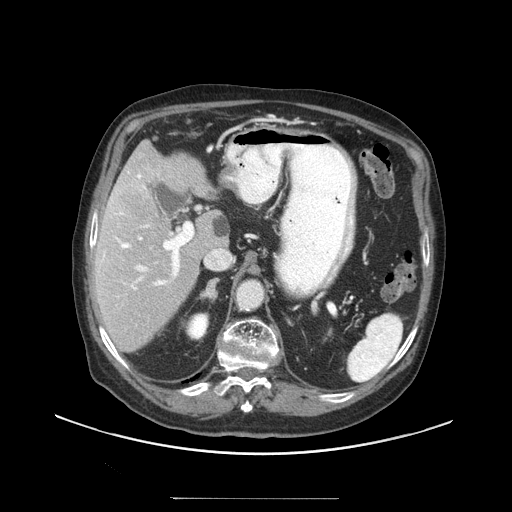
Contrast-enhanced abdominal CT (liver protocol), one axial slice. Position 62 of 97 along the scan axis. Soft-tissue window (W 400 / L 40 HU). 512 × 512 image matrix, field of view 450 × 450 mm. Case-level facts recorded for this patient, not image findings: diagnosis: hepatocellular carcinoma (patient treated with transarterial chemoembolisation; whether this scan precedes or follows treatment is not stated here); TNM stage (as recorded): Stage-IIIC; Child-Pugh class: A; tumour differentiation: well differentiated; tumour nodularity: uninodular.
Outlined on this slice (semi-automatically segmented with operator editing):
- liver parenchyma outside the tumour (the mass and vessels are separate outlines, so this box may not span the whole liver): box from (x=92, y=140) to (x=228, y=352) px
- mass: (x=122, y=191)–(x=156, y=223)
- liver vessels: (x=101, y=173)–(x=180, y=290)